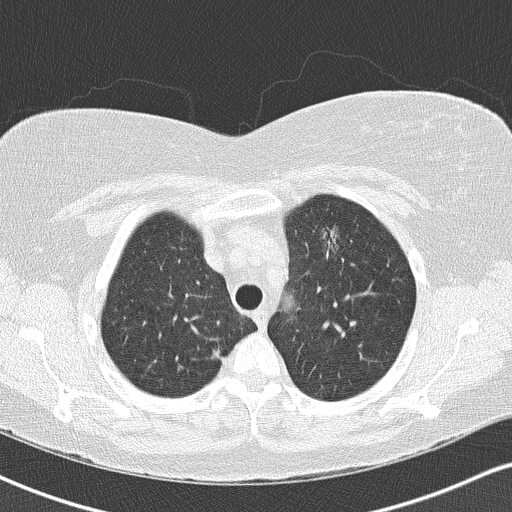
Low-dose screening chest CT, one axial slice. Position 116 of 146 along the scan axis. 120 kVp. Lung window (W 1500 / L -600 HU). 2 mm slice thickness. 512 × 512 image matrix, field of view 328 × 328 mm.
Annotated regions visible in this slice (expert manual segmentation):
- lesion 1 (tumor, upper lobe of left lung): bounding box (x1, y1, x2, y2) in pixels: (323, 224, 340, 261)